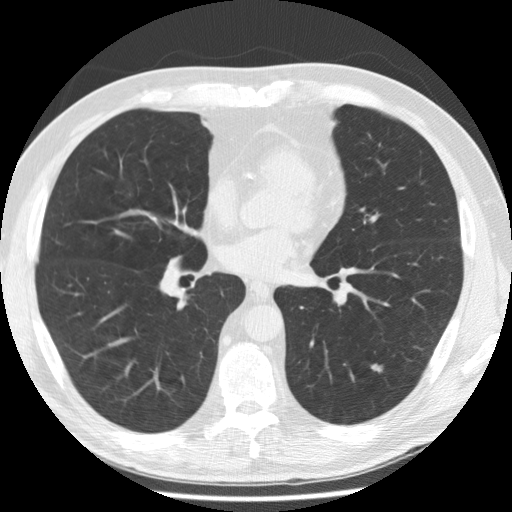
Chest CT (low-dose screening protocol), one axial image; second annual screen; lung window (W 1500 / L -600 HU); 2.5 mm slice thickness; 120 kVp. Male, age 58 years at enrolment. Former smoker at enrolment.
- Lesion marked by an expert reader, bounding box <357,351,394,384> (left, top, right, bottom; pixels).
- Screening reader's record for this exam (one nodule recorded; not confirmed to be the boxed lesion): non-calcified nodule or mass ≥4 mm, left lower lobe, 7 × 4 mm, poorly defined margins, ground glass attenuation, pre-existing on the prior screen: yes; interval growth: yes.
- Official screen result: positive, change unspecified: nodule(s) >= 4 mm or enlarging nodule(s), mass(es), or other non-specific abnormalities suspicious for lung cancer.
- Later outcome: lung cancer diagnosed 407 days after this screen — adenocarcinoma, NOS, left lower lobe, poorly differentiated (G3), stage IA (AJCC 6th edition), 8 mm at pathology.